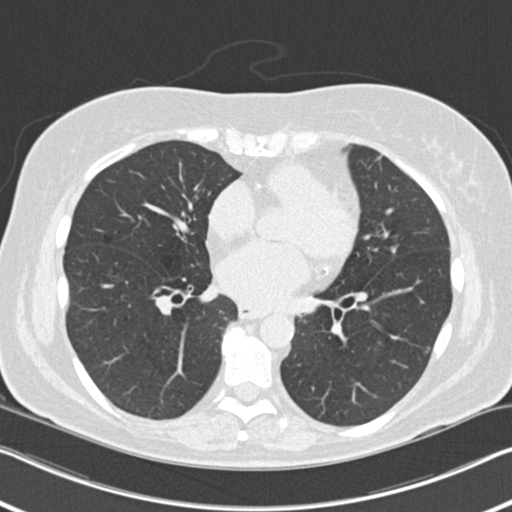
Low-dose screening chest CT, axial slice; second screening round (one year after baseline); lung window (W 1500 / L -600 HU); 2 mm slice thickness; 120 kVp; 512 × 512 image matrix. Female participant, aged 60 years at enrolment. Current smoker at enrolment.
- Expert reader's lesion annotation, bounding box [x1, y1, x2, y2] px = [376, 236, 408, 266].
- The screening reader recorded 6 non-calcified nodules or masses ≥4 mm on this exam; which of them this box marks is not recorded.
- Official screen result: positive, change unspecified: nodule(s) >= 4 mm or enlarging nodule(s), mass(es), or other non-specific abnormalities suspicious for lung cancer.